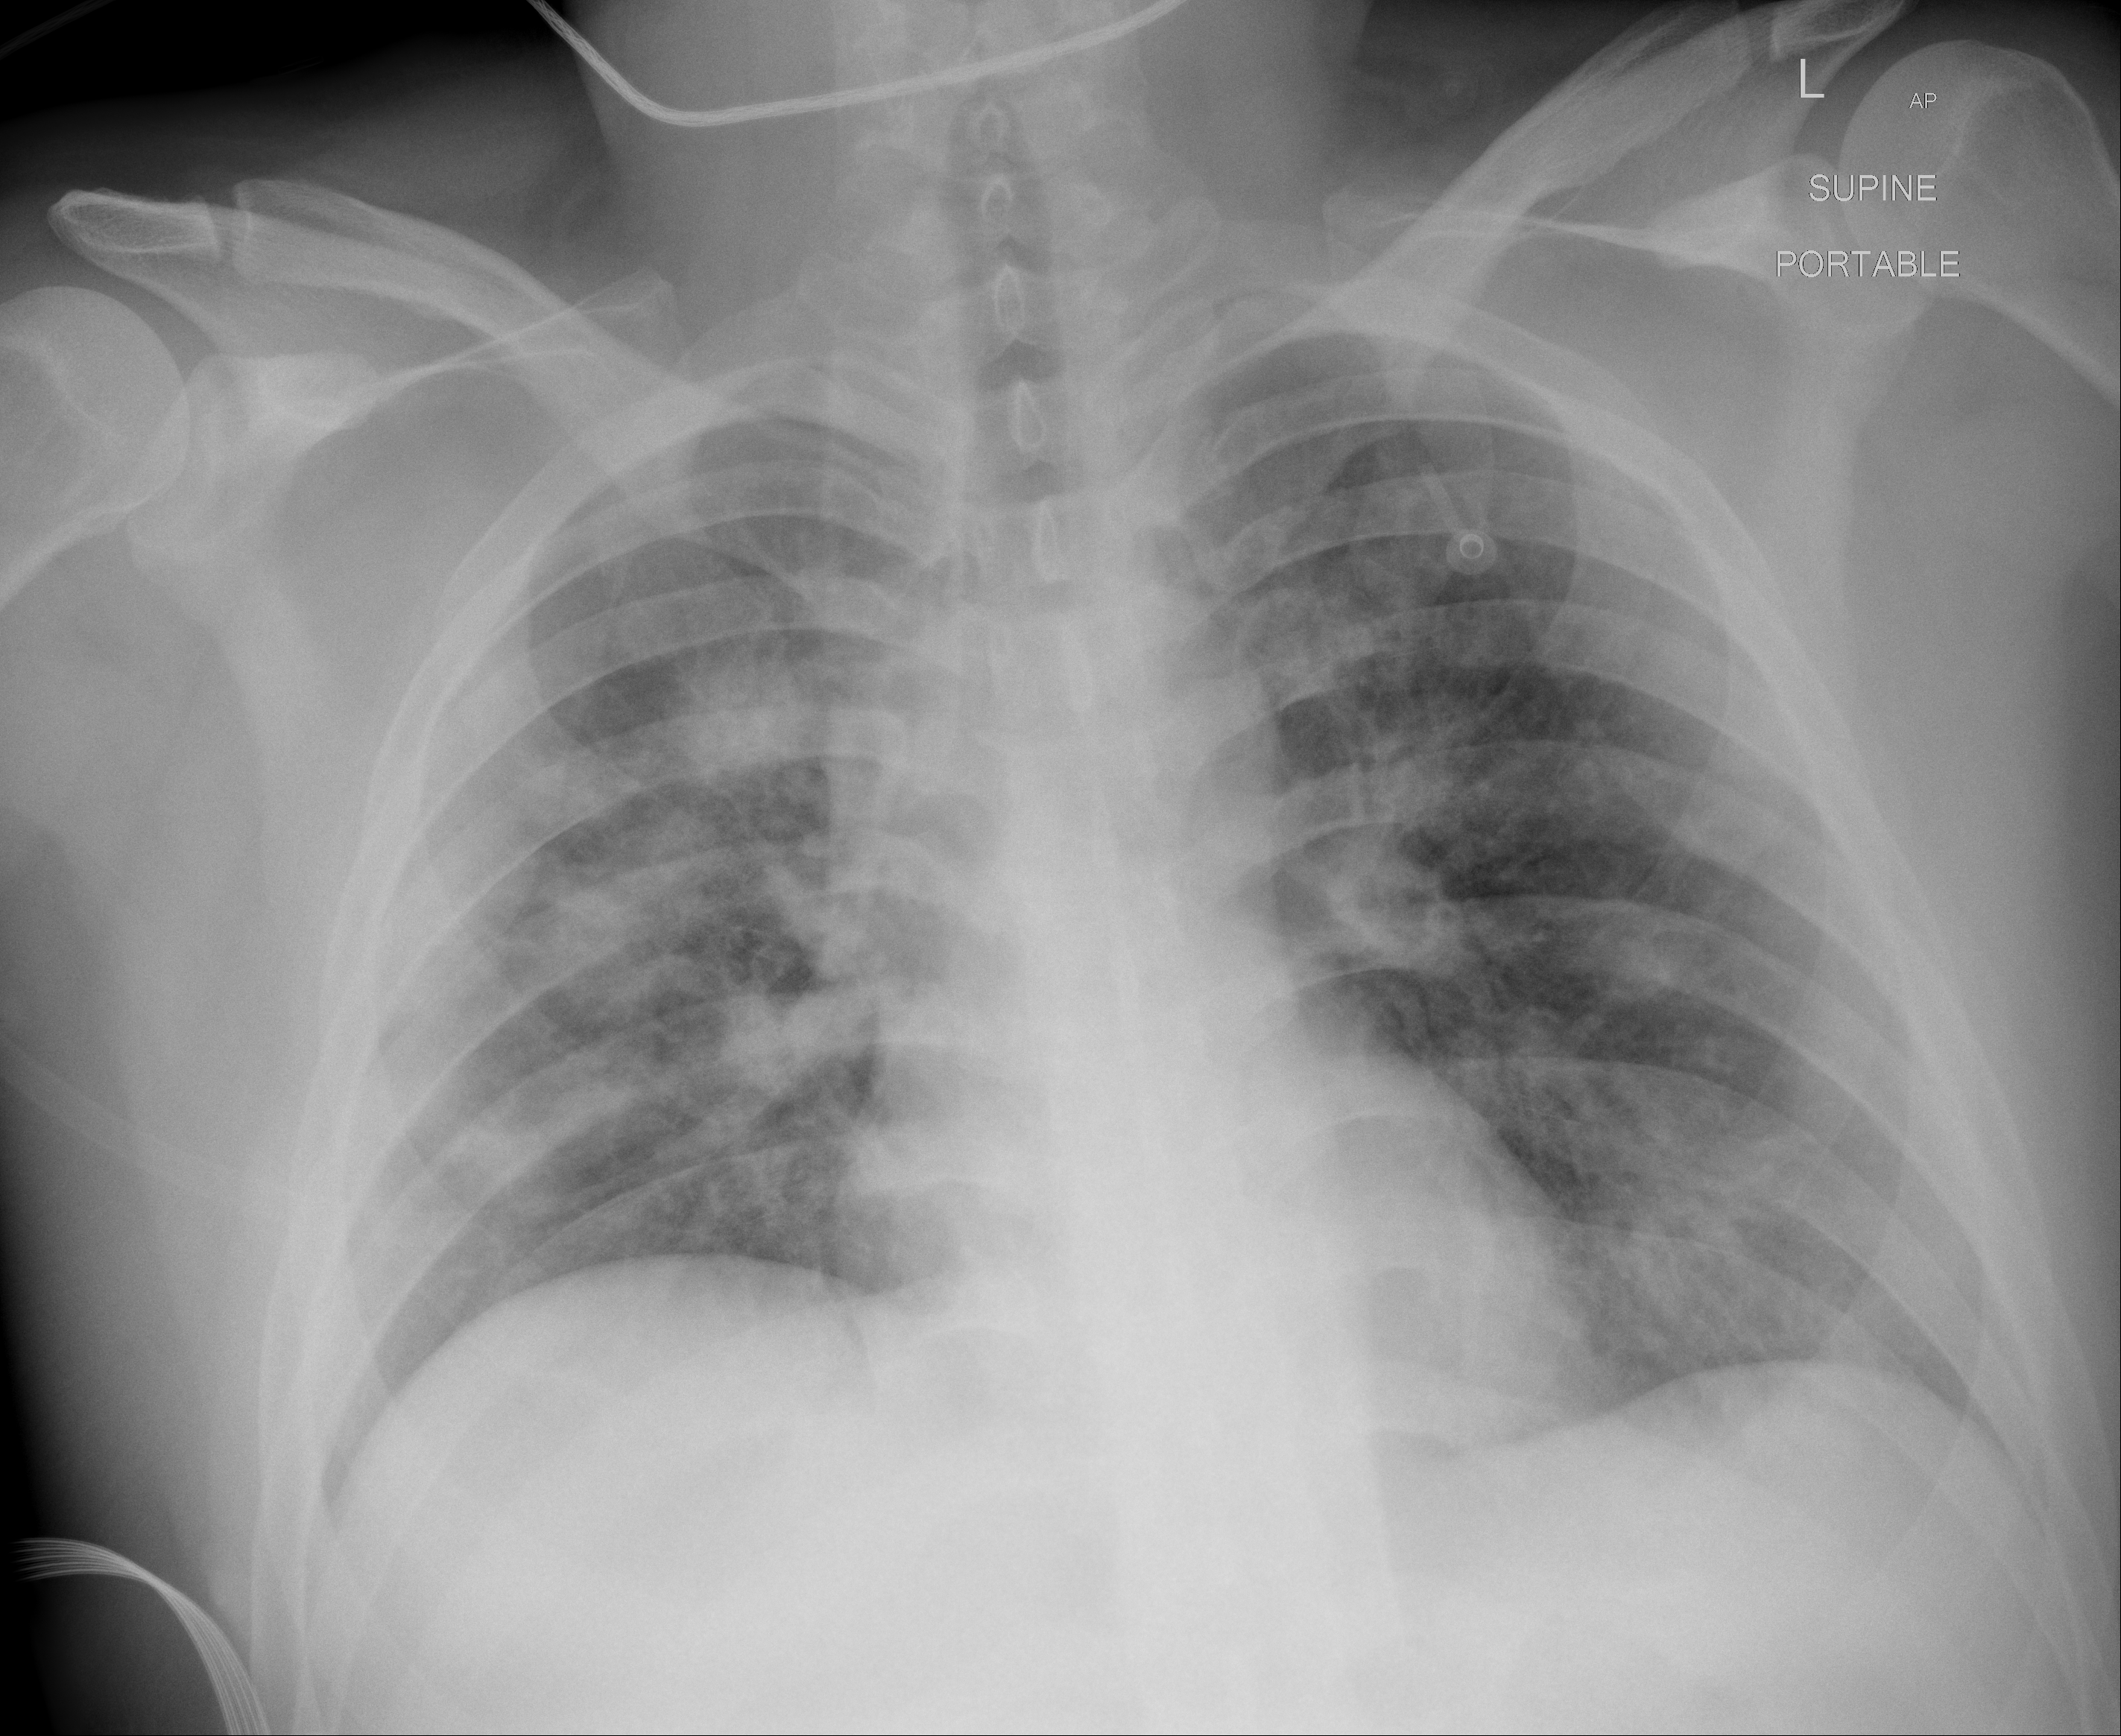
Chest X-ray, AP projection. Male patient, age 38 years; COVID-19 (test-positive).
Radiologist key findings (as recorded): worsening patchy areas of consolidation in the mid to upper portions of the right lung and to a lesser extent the lower left lung.